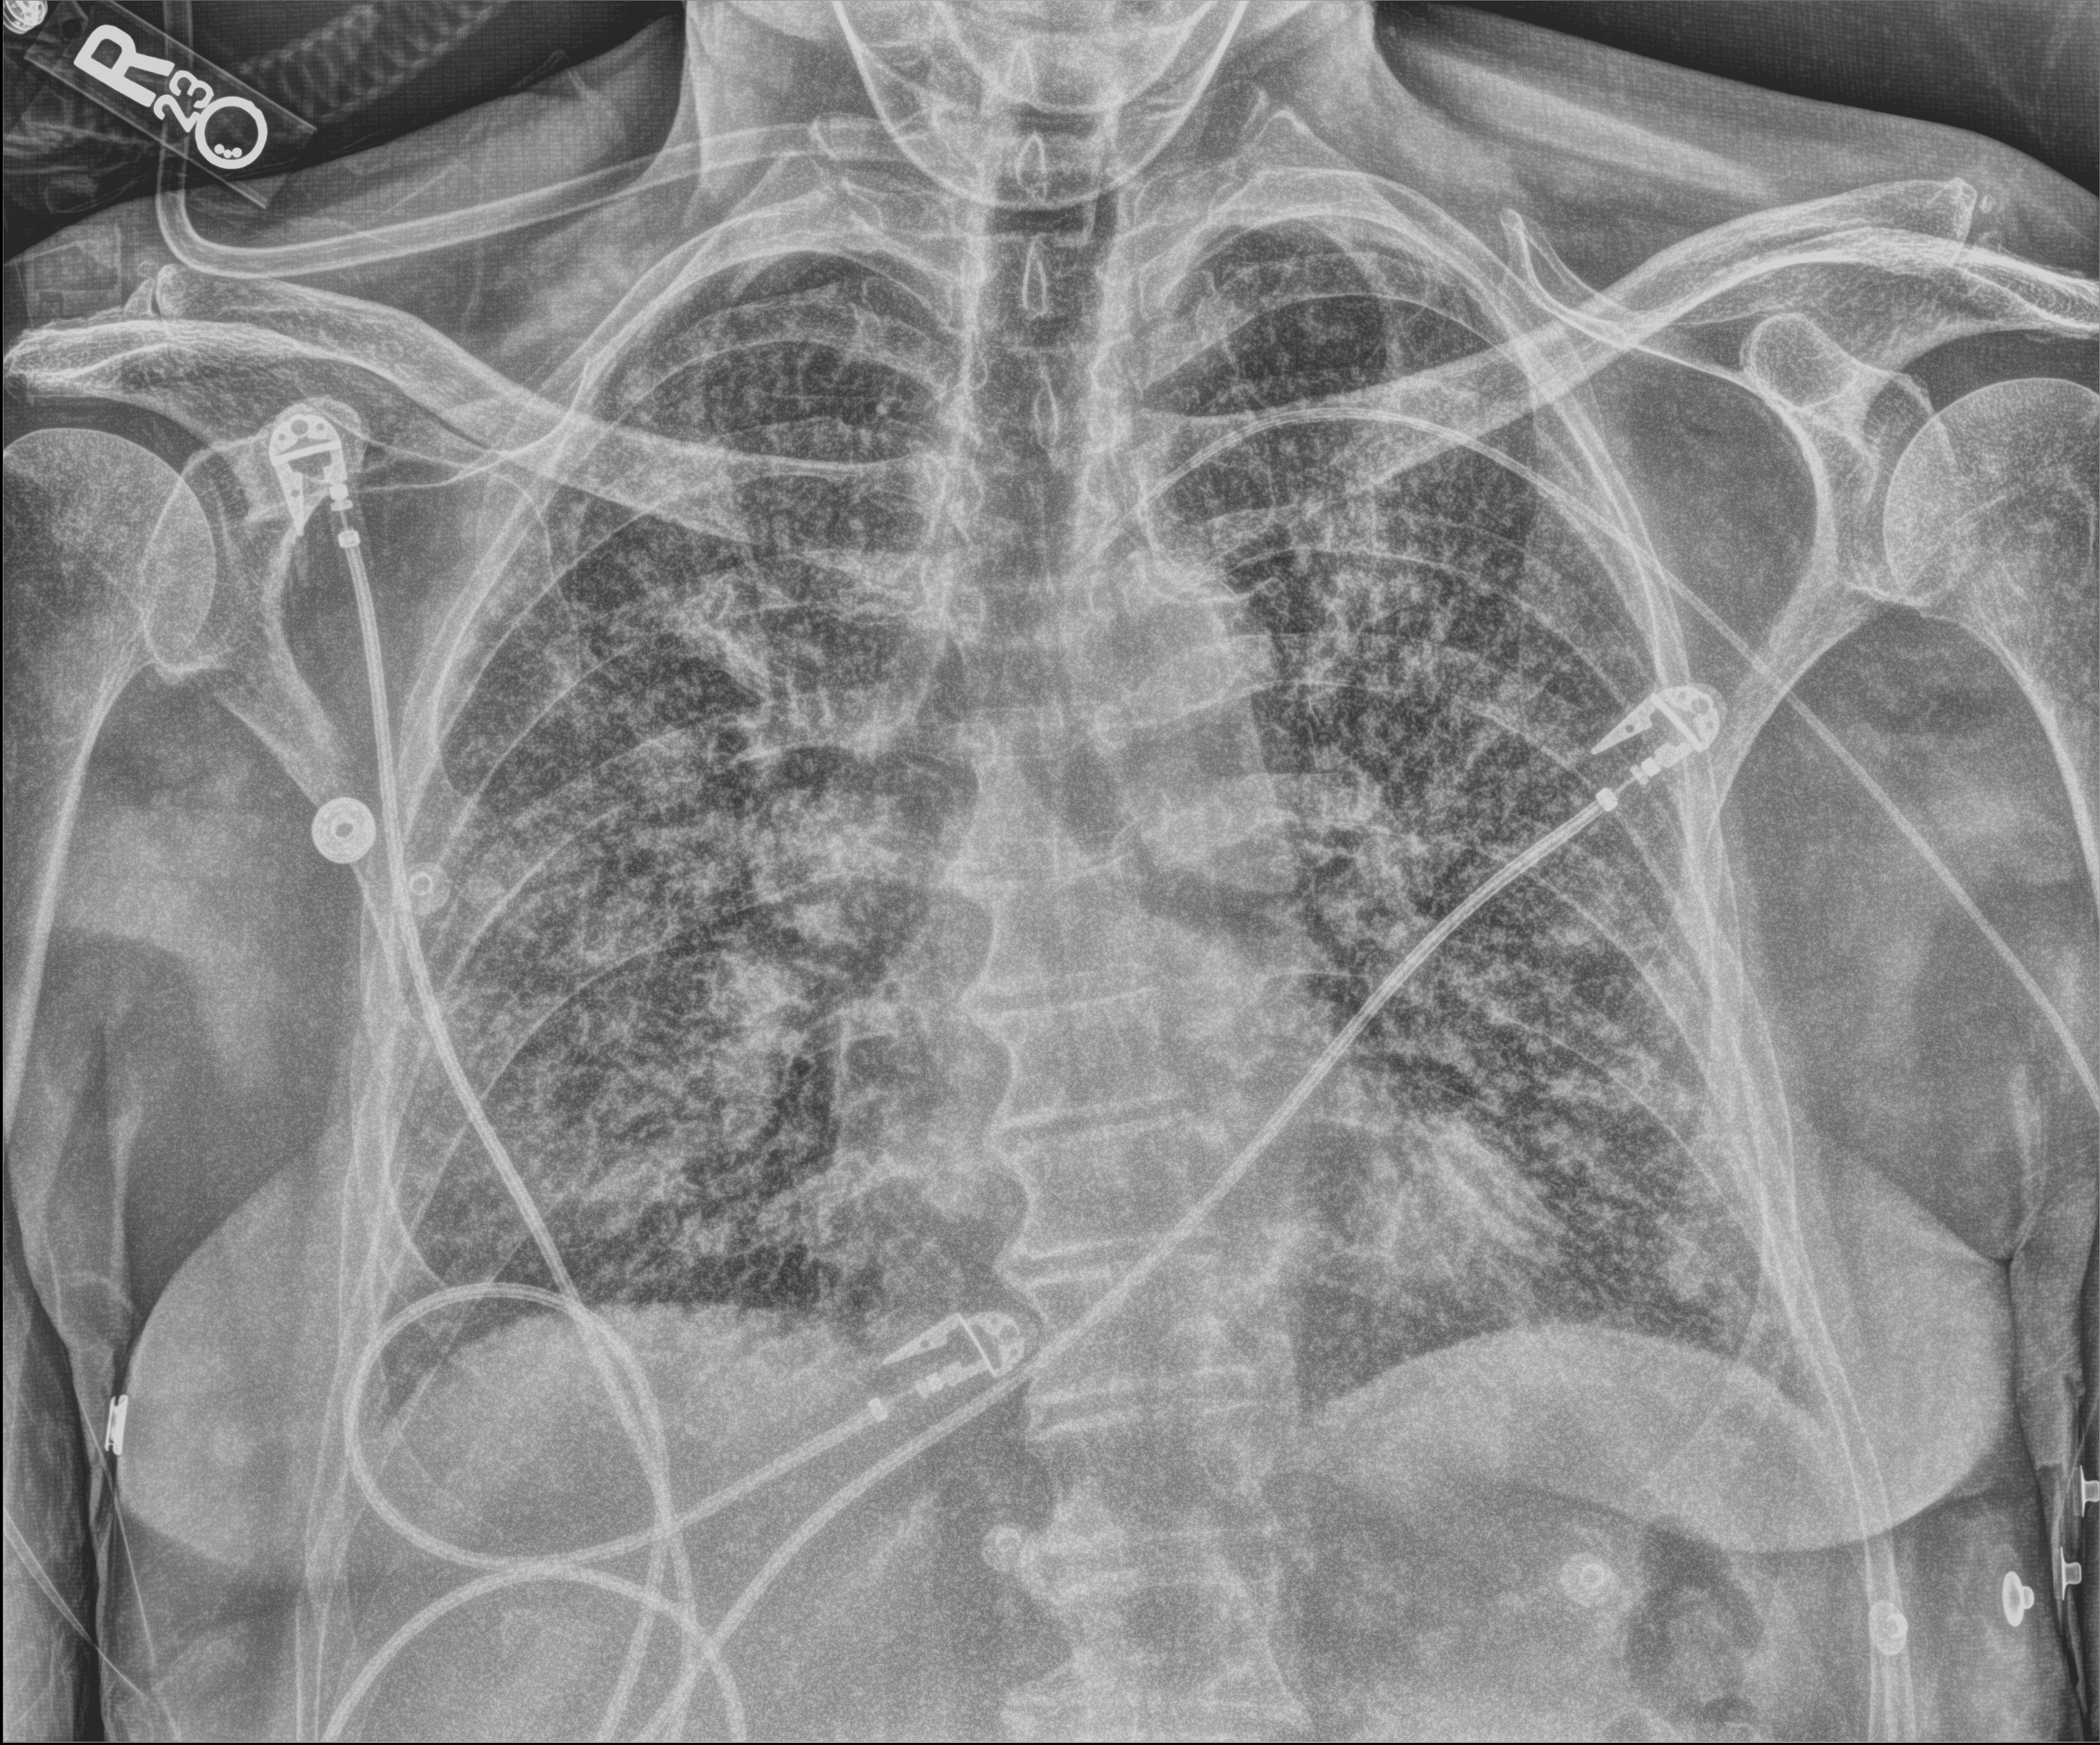
Bedside chest radiograph (computed radiography). Patient hospitalised with COVID-19; male, aged 75–90 years.
From the hospital-stay record, not from the radiograph (when in the stay this image was taken is not recorded): mechanically ventilated during this hospital stay: yes.